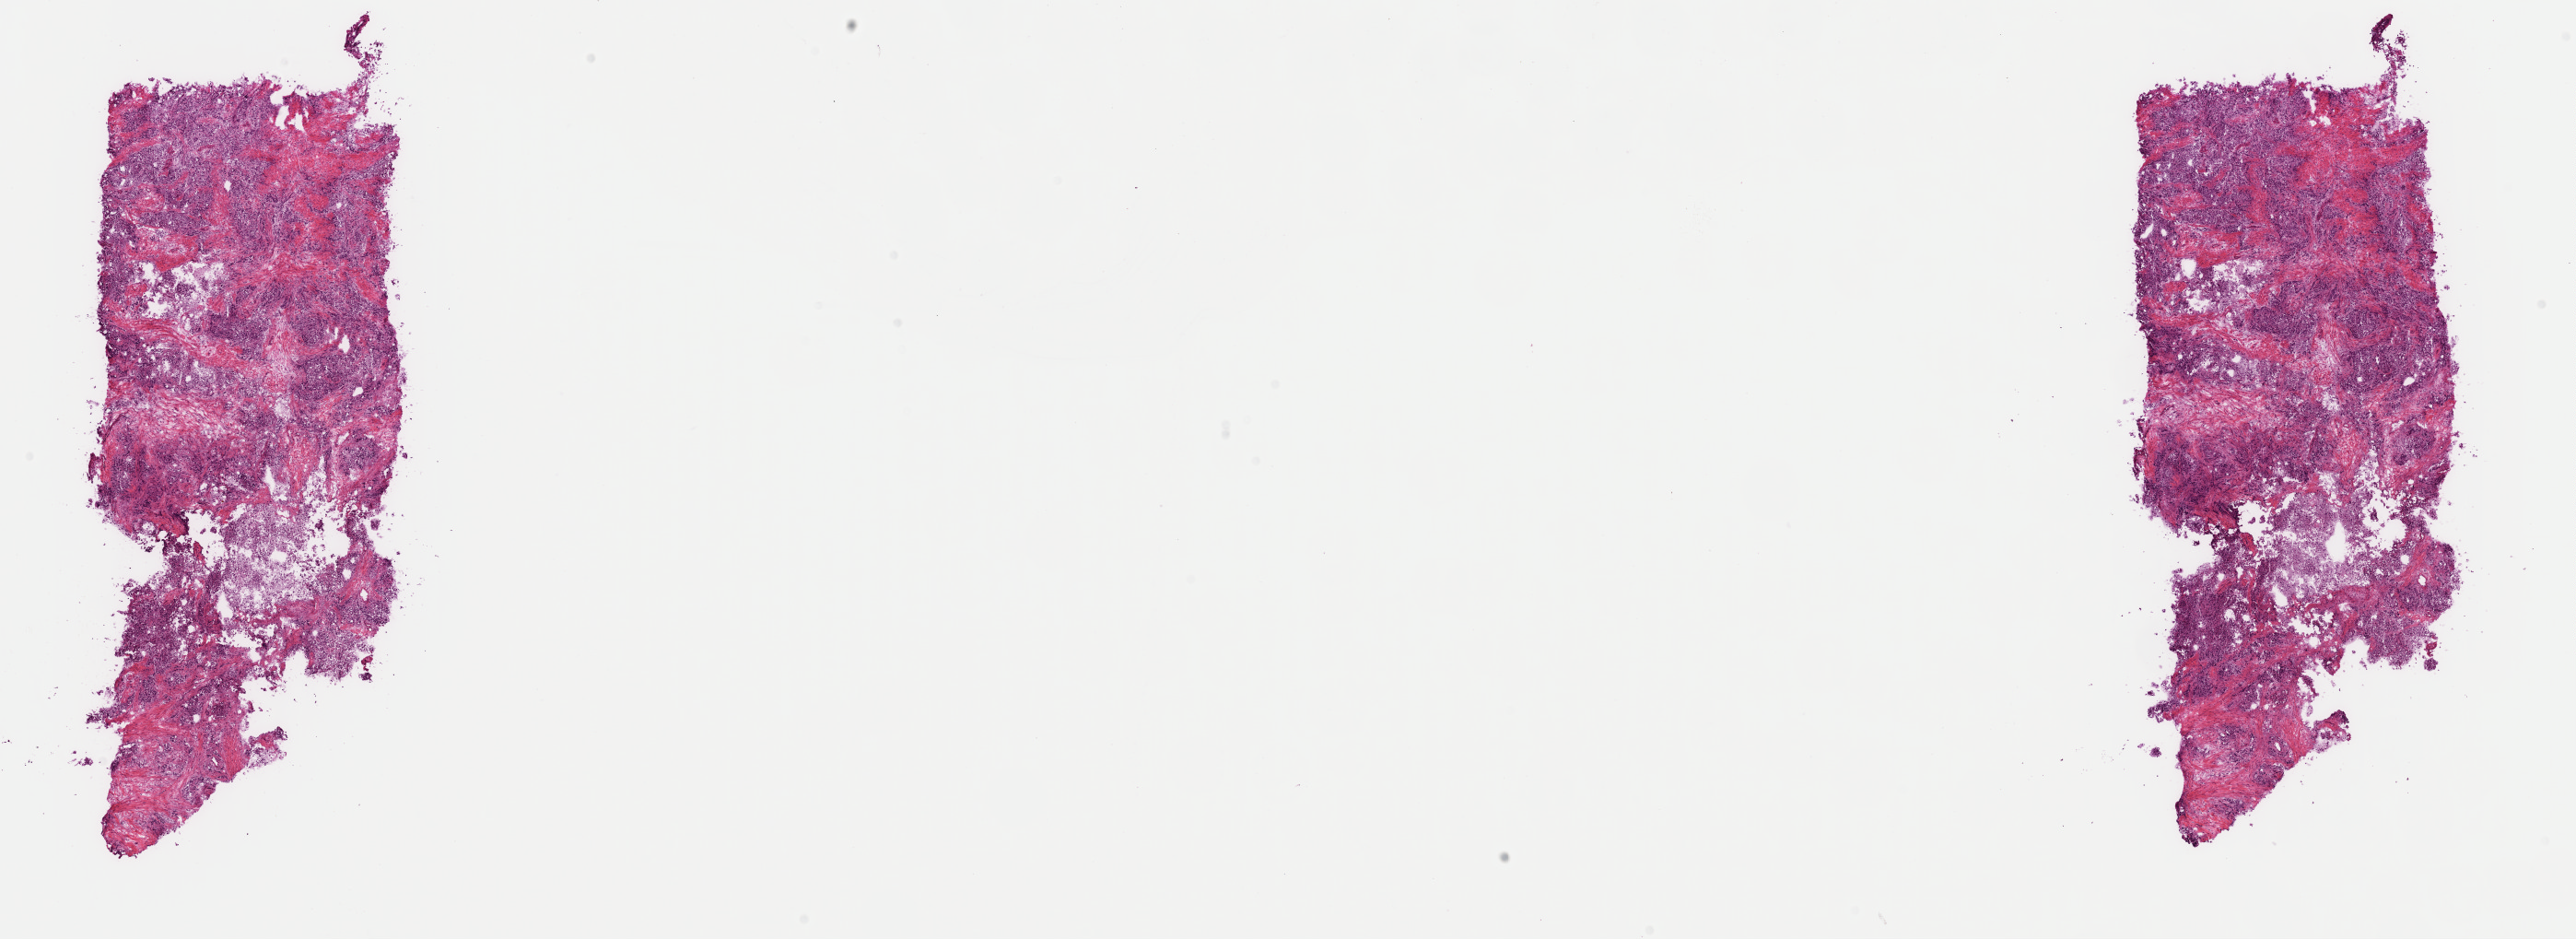
H&E-stained whole-slide image — shown as a low-resolution overview of the whole scanned area (about 22.1 x 8.0 mm, from a 40x scan), frozen section from the top of the tissue portion, primary tumour sample from the adrenal gland. Patient: male, age at initial diagnosis 67 years. Pathologist review of this section (percent, as recorded): tumour cells 80%, tumour nuclei 80%, normal cells 0%, stromal cells 20%, necrosis 0%. Infiltration values recorded for this section: lymphocyte infiltration 0%, monocyte infiltration 0%, neutrophil infiltration 0%.
- pathologic diagnosis: Malignant lymphoma, non-Hodgkin, NOS (lymph node, NOS)